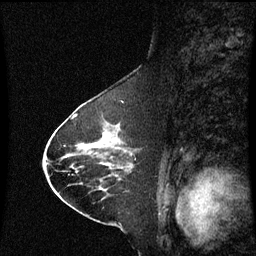
Breast MRI (dynamic contrast-enhanced), one sagittal slice. Position 33 of 60 along the scan axis. Dynamic contrast-enhanced series, image 2 of 3 at this slice position (ordered by acquisition). 1.5 T. TE 4.2 ms, TR 8.9 ms. 256 × 256 image matrix. Female patient, age 63 years. From the clinical record (not read from this slice): setting: breast cancer imaged before/during neoadjuvant chemotherapy; receptor status: HR-positive, HER2-negative.
Structures marked on this image (semi-automatically segmented with operator editing):
- analysis volume of interest (the breast-tissue region the enhancement analysis was run in; not a lesion): bounding box <94,122,134,177> (left, top, right, bottom; pixels)
- tumour enhancement mask (voxels above the 70 % enhancement threshold inside the analysis volume of interest): <104,134,107,137>